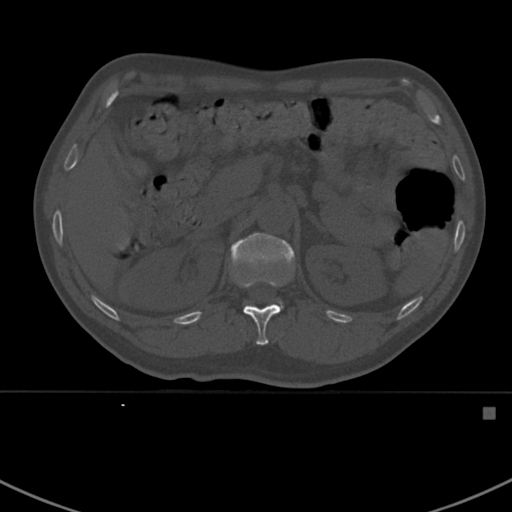
CT including the spine, one axial slice. Slice 322 of 412 in the series (ordered by position). Bone window (W 1800 / L 400 HU). 1.5 mm slice thickness. 512 × 512 image matrix. Patient: male, 59 years. Case-level facts recorded for this patient, not image findings: primary cancer: prostate.
Outlined on this slice (semi-automatically segmented with operator editing):
- L1 vertebra: bounding box (x1, y1, x2, y2) in pixels: (230, 233, 295, 309)
- T12 vertebra: (240, 279, 282, 346)